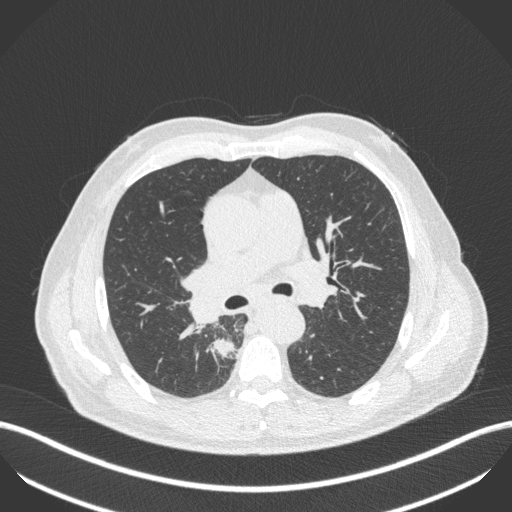
Chest CT, one axial slice. Position 282 of 451 along the scan axis. Reconstruction kernel B31f. 100 kVp. Lung window (W 1500 / L -600 HU). 1 mm slice thickness. 512 × 512 image matrix, field of view 400 × 400 mm. Patient: male, 61 years. From the clinical record (not read from this slice): clinical TNM (as recorded): T1 N0 M0.
Structures marked on this image (rectangle marked by the reading radiologist):
- lung tumour (recorded histology: small cell carcinoma): bounding box <209,338,238,363> (left, top, right, bottom; pixels)